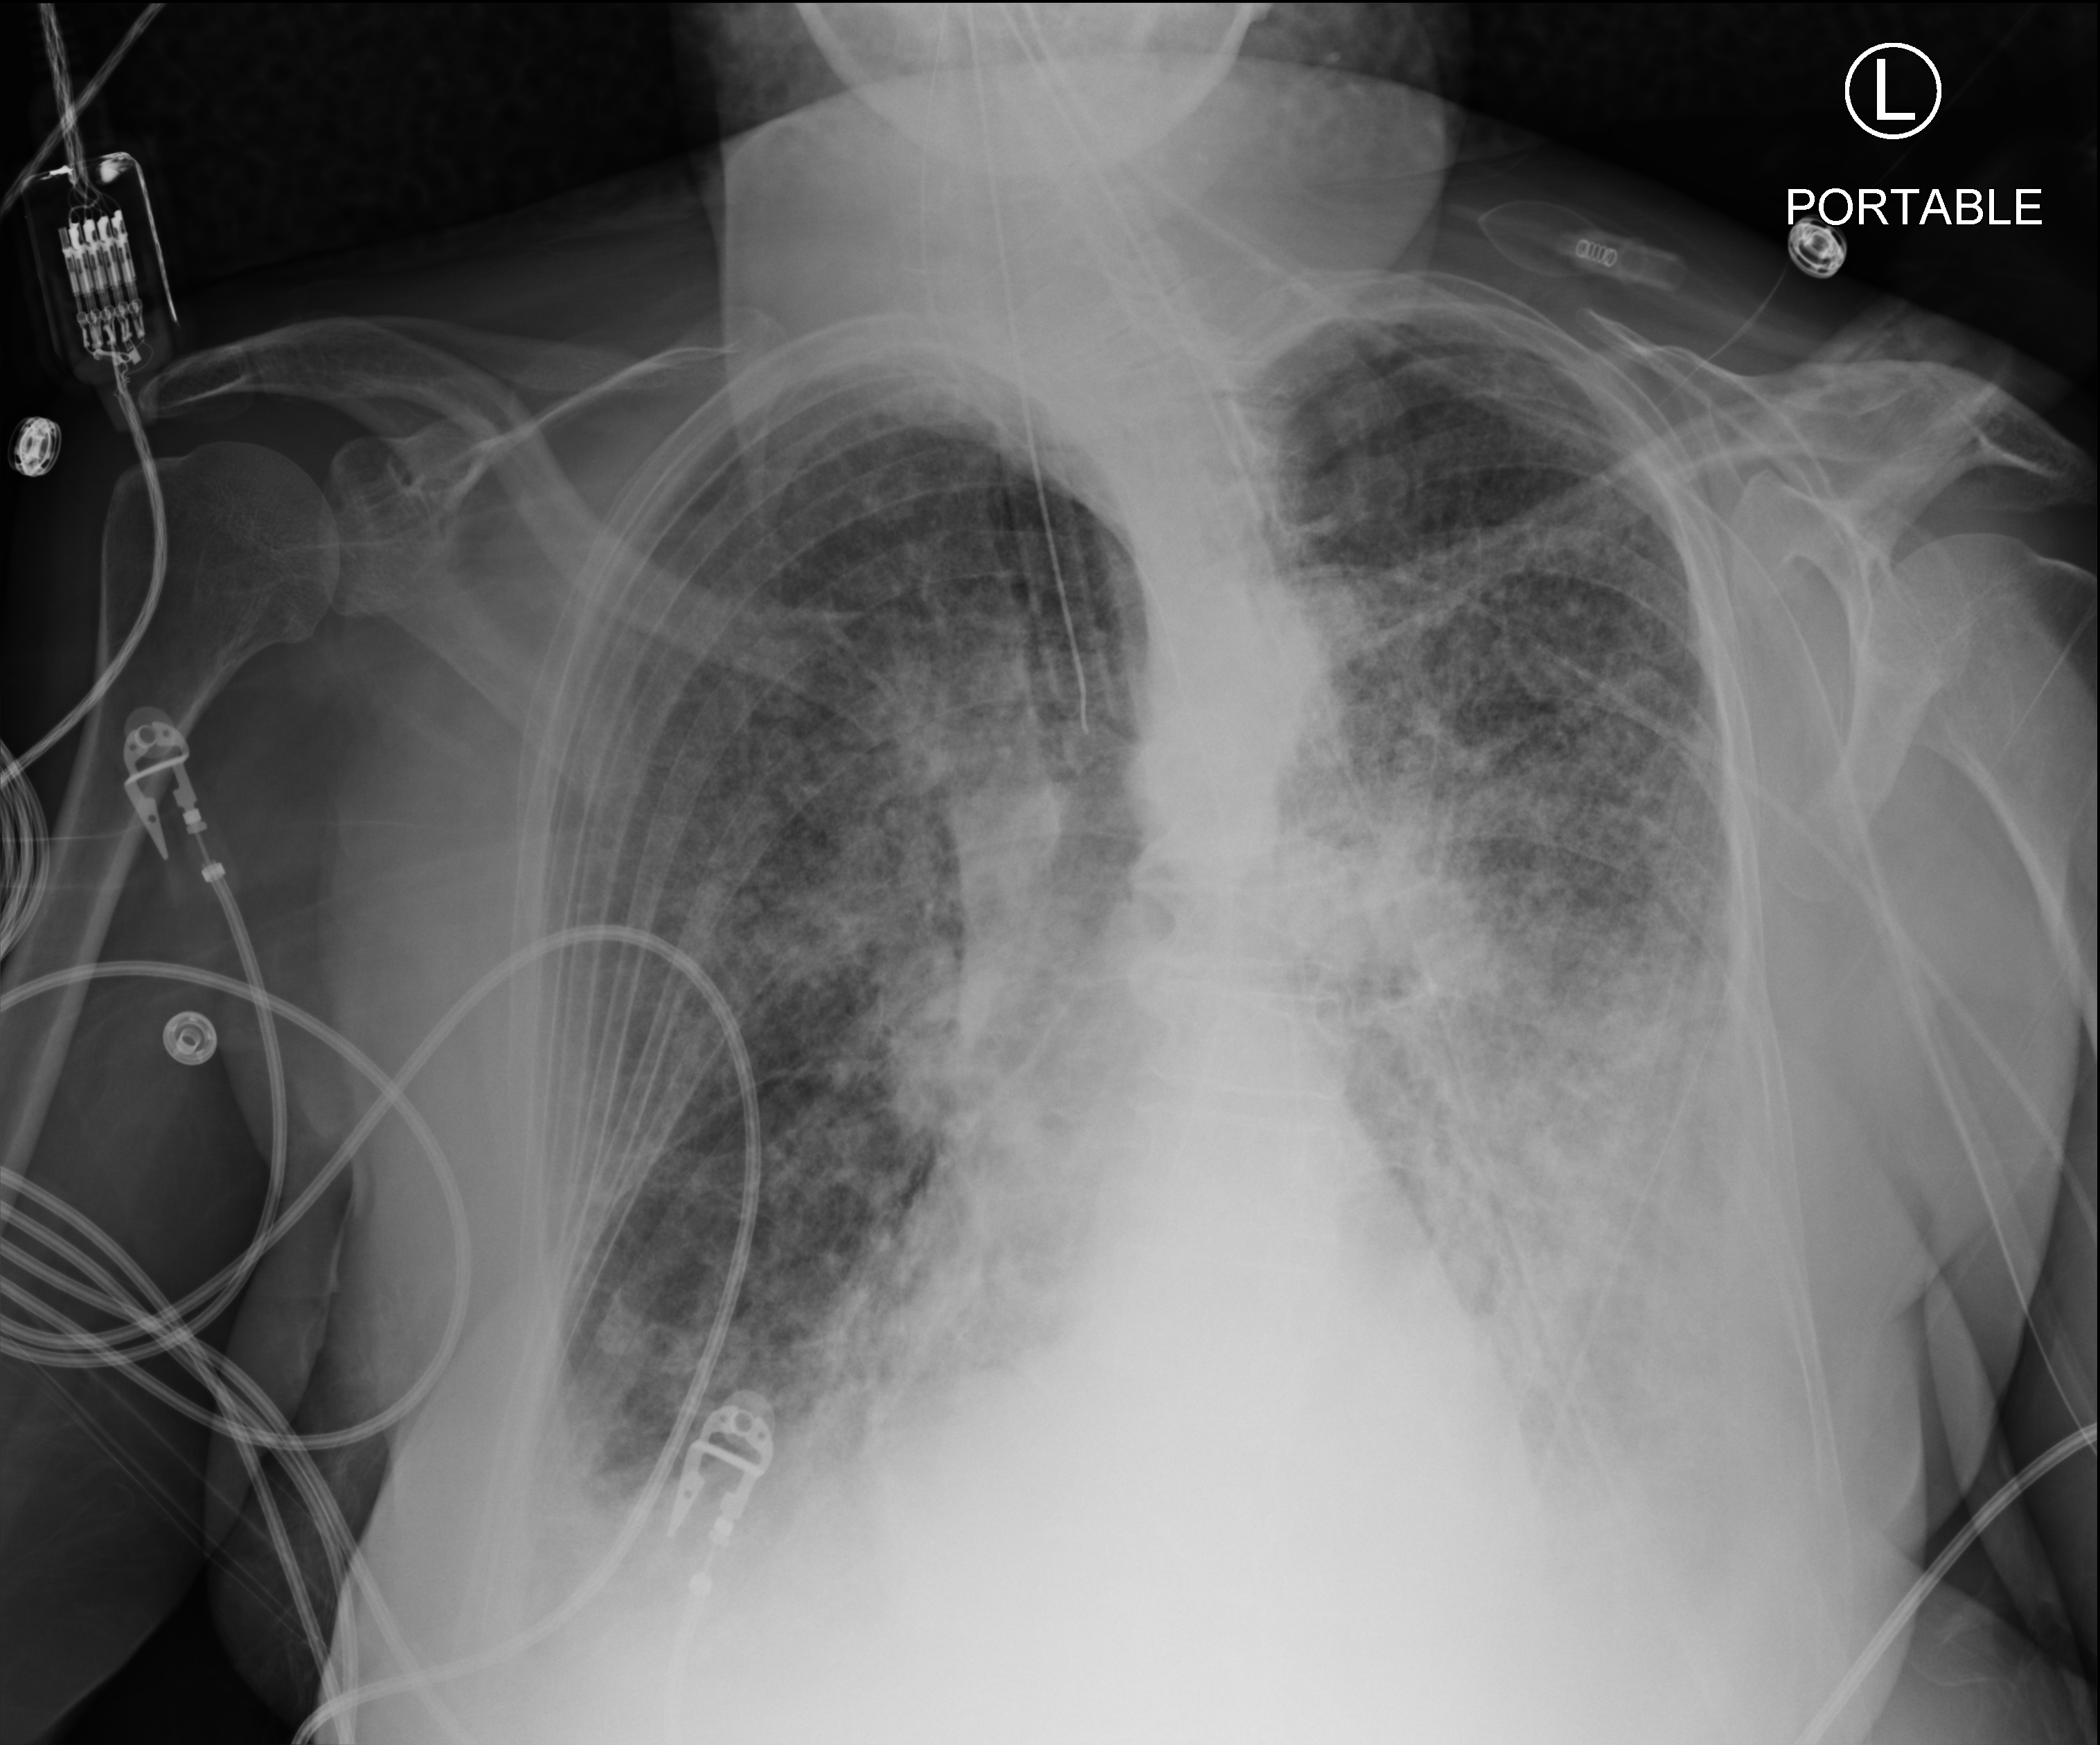
Bedside chest radiograph (computed radiography). Female patient hospitalised with COVID-19, age 75–90 years.
From the hospital-stay record, not from the radiograph (when in the stay this image was taken is not recorded): length of hospital stay: 70 days; admitted to intensive care during this hospital stay: yes; mechanically ventilated during this hospital stay: yes.